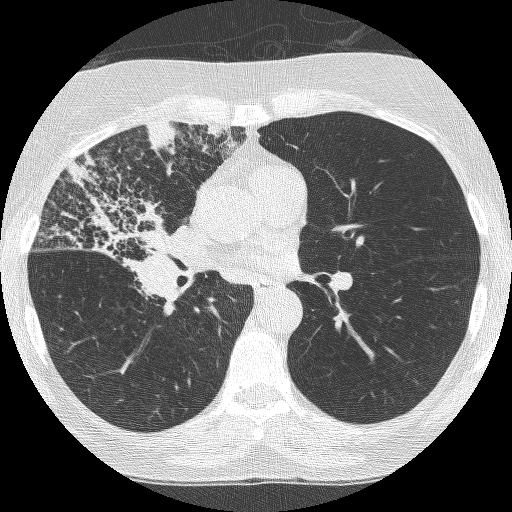
Chest CT (low-dose screening protocol), one axial image, third annual screen, lung window (W 1500 / L -600 HU), lung (sharp) reconstruction kernel (BONE), 120 kVp. Female participant, aged 64 years at enrolment. Former smoker at enrolment.
Lesion marked by an expert reader, bounding box <62,172,201,313> (left, top, right, bottom; pixels). Screening reader's record for this exam (one nodule recorded; not confirmed to be the boxed lesion): non-calcified nodule or mass ≥4 mm, right upper lobe, 49 × 43 mm, spiculated (stellate) margins, soft tissue attenuation, pre-existing on the prior screen: yes; interval growth: yes. Participant outcome: lung cancer diagnosed 7 days after this screen — adenocarcinoma, NOS, right upper lobe, right middle lobe, right hilum, stage IV (AJCC 6th edition), 85 mm at pathology.